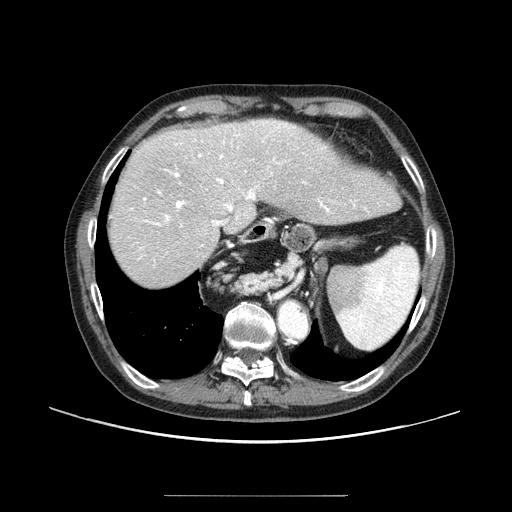
Contrast-enhanced abdominal CT (liver protocol), one axial slice. Slice 70 of 91 in the series (ordered by position). Reconstruction kernel STANDARD. One of 2 acquisitions stored at this slice position. Soft-tissue window (W 400 / L 40 HU). 2.5 mm slice thickness. 512 × 512 image matrix, field of view 400 × 400 mm. Case-level facts recorded for this patient, not image findings: diagnosis: hepatocellular carcinoma (patient treated with transarterial chemoembolisation; whether this scan precedes or follows treatment is not stated here); TNM stage (as recorded): Stage-I; Child-Pugh class: A; tumour differentiation: moderately differentiated.
Annotated regions visible in this slice (semi-automatically segmented with operator editing):
- abdominal aorta: bounding box [x1, y1, x2, y2] px = [279, 303, 307, 338]
- liver parenchyma outside the tumour (the mass and vessels are separate outlines, so this box may not span the whole liver): [108, 118, 394, 286]
- liver vessels: [138, 121, 368, 260]